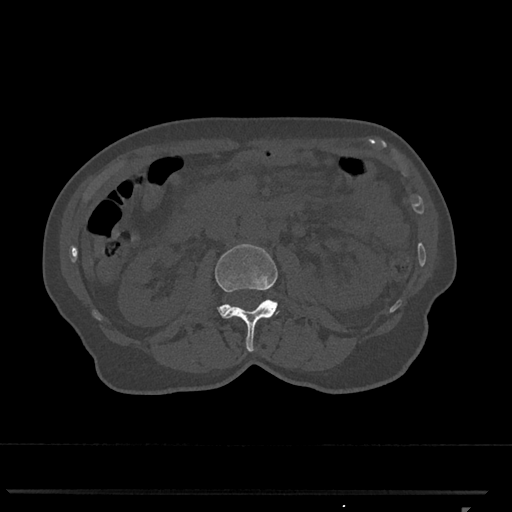
CT including the spine, one axial slice; slice 330 of 793 in the series (ordered by position); reconstruction kernel Br40s/3; 120 kVp; bone window (W 1800 / L 400 HU); 0.5 mm slice thickness; 512 × 512 image matrix, field of view 380 × 380 mm. Patient: female, 62 years. Case-level facts recorded for this patient, not image findings: primary cancer: renal.
Structures marked on this image (semi-automatically segmented with operator editing):
- L2 vertebra: box from (x=215, y=244) to (x=279, y=351) px